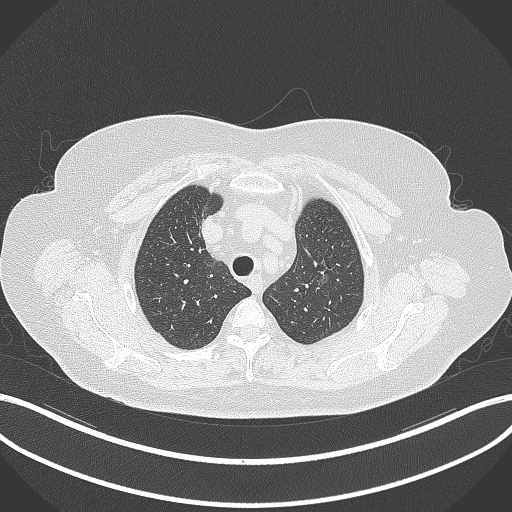
Chest CT, one axial slice; slice 275 of 309 in the series (ordered by position); lung window (W 1500 / L -600 HU); 1 mm slice thickness; 512 × 512 image matrix. Female patient, age 70 years. Case-level facts recorded for this patient, not image findings: clinical TNM (as recorded): T1c N0 M0.
Annotated regions visible in this slice (rectangle marked by the reading radiologist):
- lung tumour (recorded histology: adenocarcinoma): bounding box (x1, y1, x2, y2) in pixels: (315, 261, 337, 296)